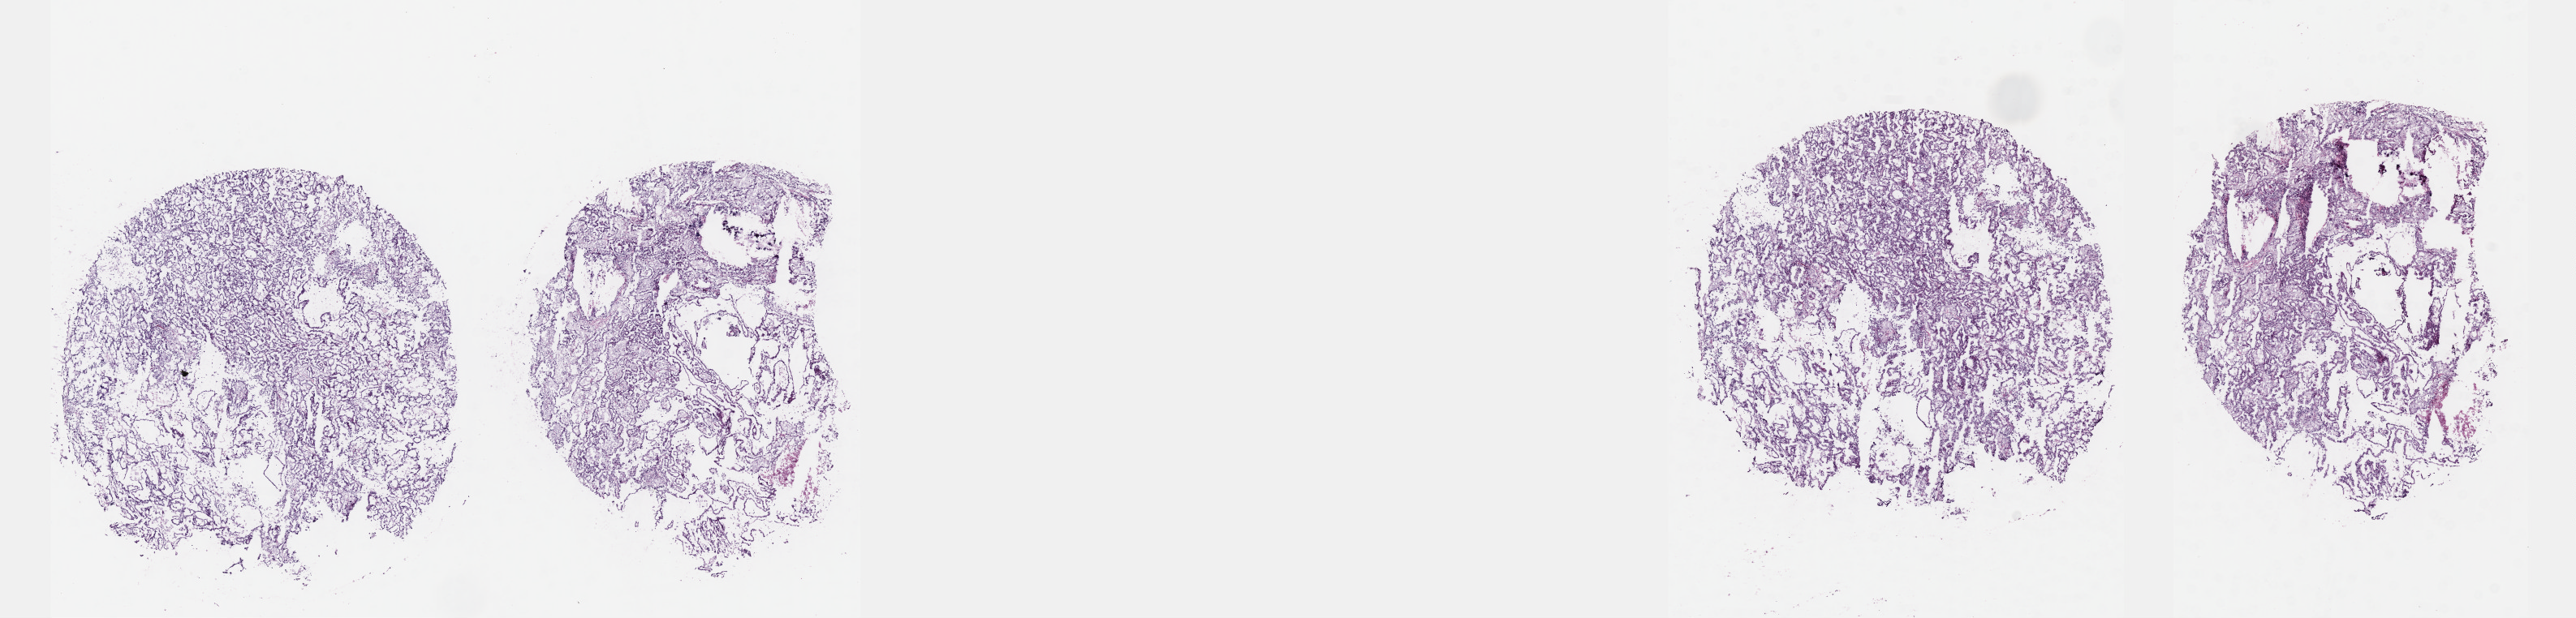
Hematoxylin and eosin (H&E) stained whole-slide image, a low-resolution overview of the entire scanned area, about 25.7 x 6.2 mm (slide scanned at 40x), frozen section from the top of the tissue portion, primary tumour sample from the kidney. Male, age 53 years at initial diagnosis. Slide review estimates, as recorded: tumour cells 90%, tumour nuclei 90%, normal cells 0%, stromal cells 10%, necrosis 0%. Inflammatory infiltration, as recorded: lymphocyte infiltration 0%, monocyte infiltration 0%, neutrophil infiltration 0%.
* diagnosis: Papillary adenocarcinoma, NOS